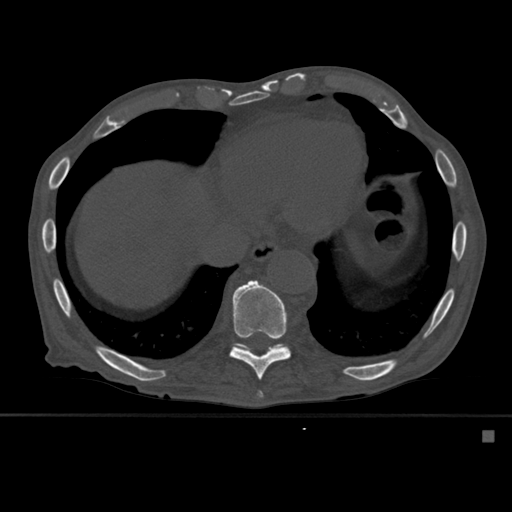
CT including the spine, one axial slice. Position 313 of 527 along the scan axis. Bone window (W 1800 / L 400 HU). 1.5 mm slice thickness. 512 × 512 image matrix. Patient: male, 78 years. Case-level facts recorded for this patient, not image findings: primary cancer: prostate.
Annotated regions visible in this slice (semi-automatically segmented with operator editing):
- T10 vertebra: bounding box (x1, y1, x2, y2) in pixels: (229, 280, 291, 380)
- T11 vertebra: (235, 338, 290, 353)
- T9 vertebra: (257, 391, 264, 398)